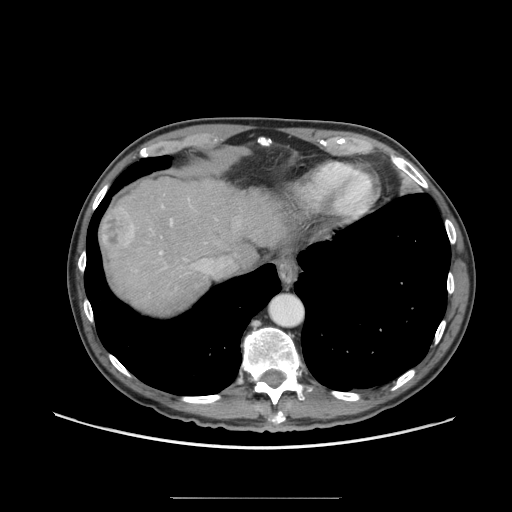
Contrast-enhanced abdominal CT (liver protocol), one axial slice. 140 kVp. Soft-tissue window (W 400 / L 40 HU). 2.5 mm slice thickness. 512 × 512 image matrix. From the clinical record (not read from this slice): diagnosis: hepatocellular carcinoma (patient treated with transarterial chemoembolisation; whether this scan precedes or follows treatment is not stated here); TNM stage (as recorded): Stage-I; Child-Pugh class: A; tumour differentiation: well differentiated.
Structures marked on this image (semi-automatically segmented with operator editing):
- abdominal aorta: bounding box [x1, y1, x2, y2] px = [270, 296, 303, 327]
- liver parenchyma outside the tumour (the mass and vessels are separate outlines, so this box may not span the whole liver): [102, 178, 290, 313]
- mass: [101, 205, 137, 251]
- liver vessels: [159, 199, 213, 274]